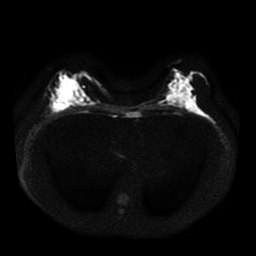
Breast MRI, one axial slice; slice 20 of 41 in the series (ordered by position); diffusion-weighted series; image 2 of 4 stored at this slice position (different b-values; order by instance number); 1.5 T; 5 mm slice thickness; 256 × 256 image matrix, field of view 330 × 330 mm. Female patient.
Structures marked on this image (outlined manually by an expert reader):
- tumour on diffusion-weighted imaging: bounding box <52,102,64,109> (left, top, right, bottom; pixels)